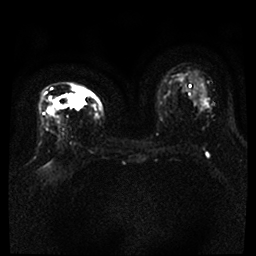
Breast MRI, one axial slice. Diffusion-weighted series; image 2 of 4 stored at this slice position (different b-values; order by instance number). 1.5 T. 4 mm slice thickness. 256 × 256 image matrix, field of view 360 × 360 mm. Female patient.
Structures marked on this image (outlined manually by an expert reader):
- tumour on diffusion-weighted imaging: bounding box <56,87,85,110> (left, top, right, bottom; pixels)